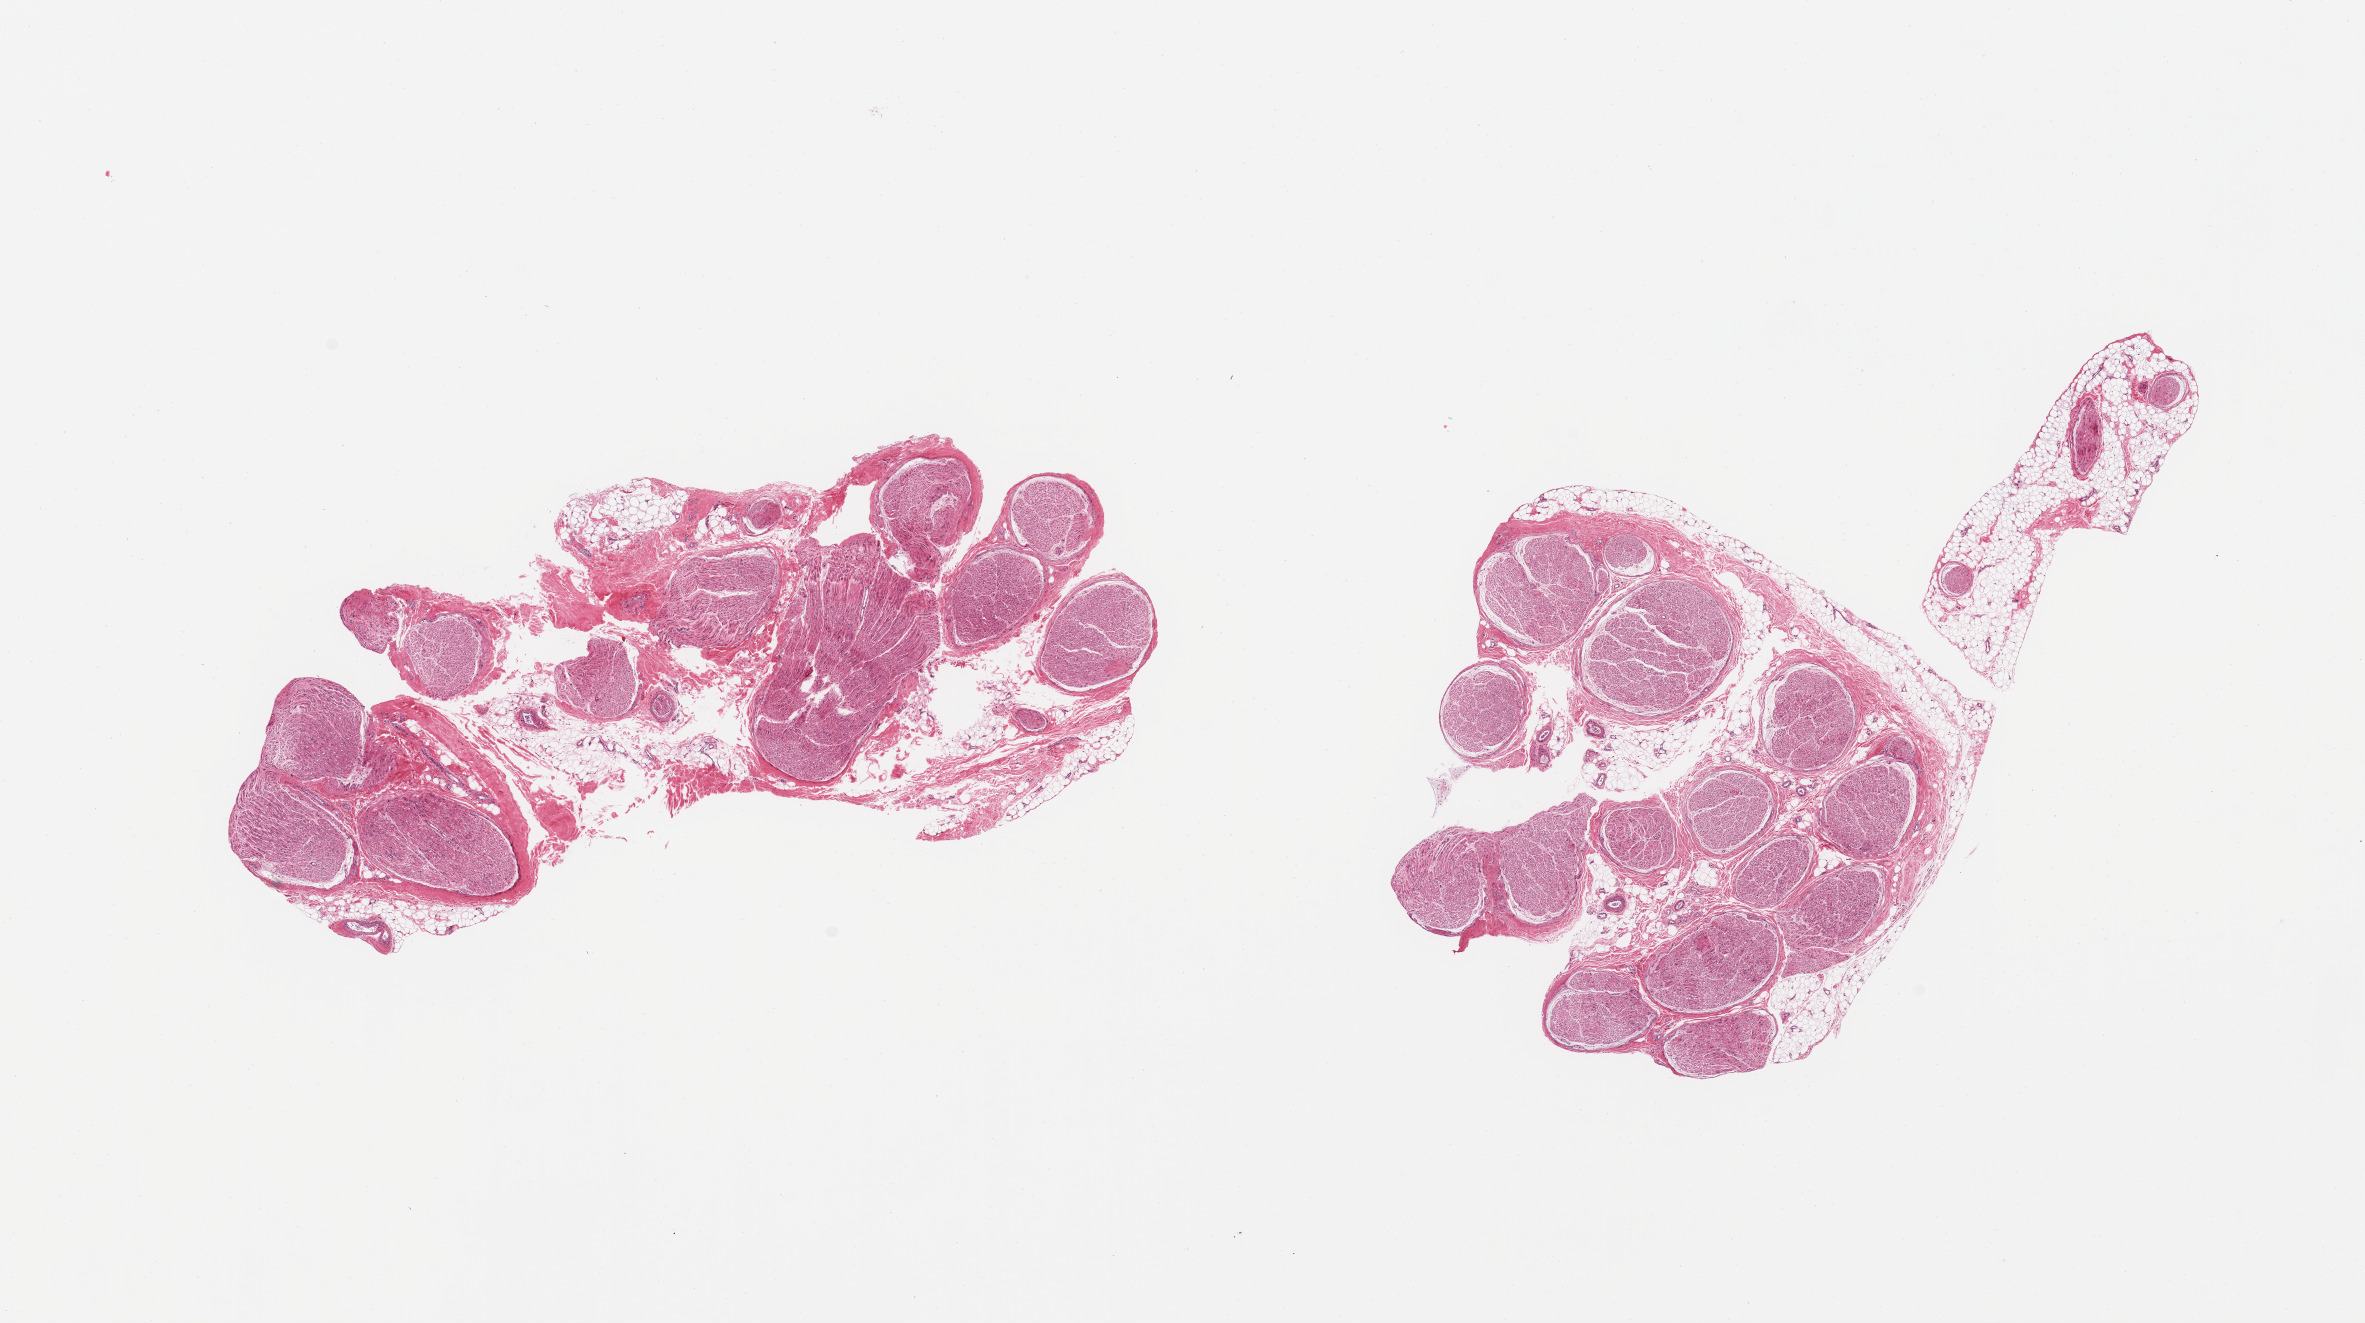
Whole-slide image, hematoxylin and eosin (H&E) stain, brightfield, a low-resolution overview of the entire scanned area, about 18.7 x 10.5 mm (from a 20x scan), PAXgene-fixed paraffin-embedded (PFPE) section, sampled site (target tissue): tibial nerve, donor tissue sample. Male donor.
Review note (as recorded): 2 pieces; includes ~20% attached and internal fat.